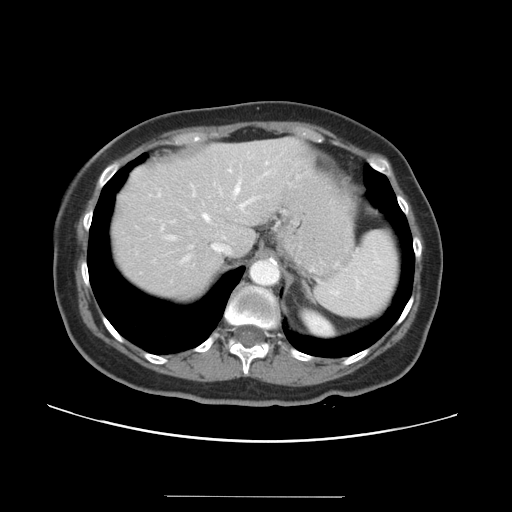
Contrast-enhanced abdominal CT, one axial slice; position 27 of 34 along the scan axis; reconstruction kernel STANDARD; intravenous contrast given; soft-tissue window (W 400 / L 40 HU); 5 mm slice thickness; 512 × 512 image matrix, field of view 382 × 382 mm. Female patient, age 69 years. Case-level facts recorded for this patient, not image findings: diagnosis: colorectal cancer liver metastases, imaged before liver resection; multiple liver metastases: yes; largest metastasis: 1.4 cm; disease in both lobes: yes.
Annotated regions visible in this slice (manually delineated by an expert):
- hepatic veins: bounding box [x1, y1, x2, y2] px = [158, 163, 267, 260]
- liver: [113, 138, 309, 300]
- planned liver remnant (the part of the liver to remain after resection): [113, 138, 309, 301]